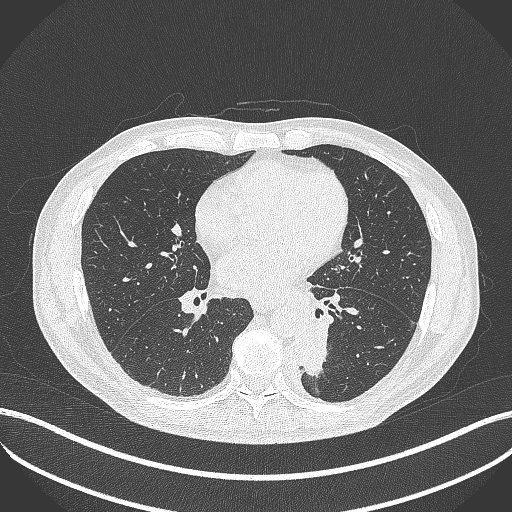
Chest CT, one axial slice; slice 187 of 451 in the series (ordered by position); 120 kVp; lung window (W 1500 / L -600 HU); 1 mm slice thickness; 512 × 512 image matrix. Patient: male, 72 years. Case-level facts recorded for this patient, not image findings: clinical TNM (as recorded): T2b N0 M1.
Annotated regions visible in this slice (rectangle marked by the reading radiologist):
- lung tumour (recorded histology: adenocarcinoma): box from (x=294, y=313) to (x=337, y=378) px